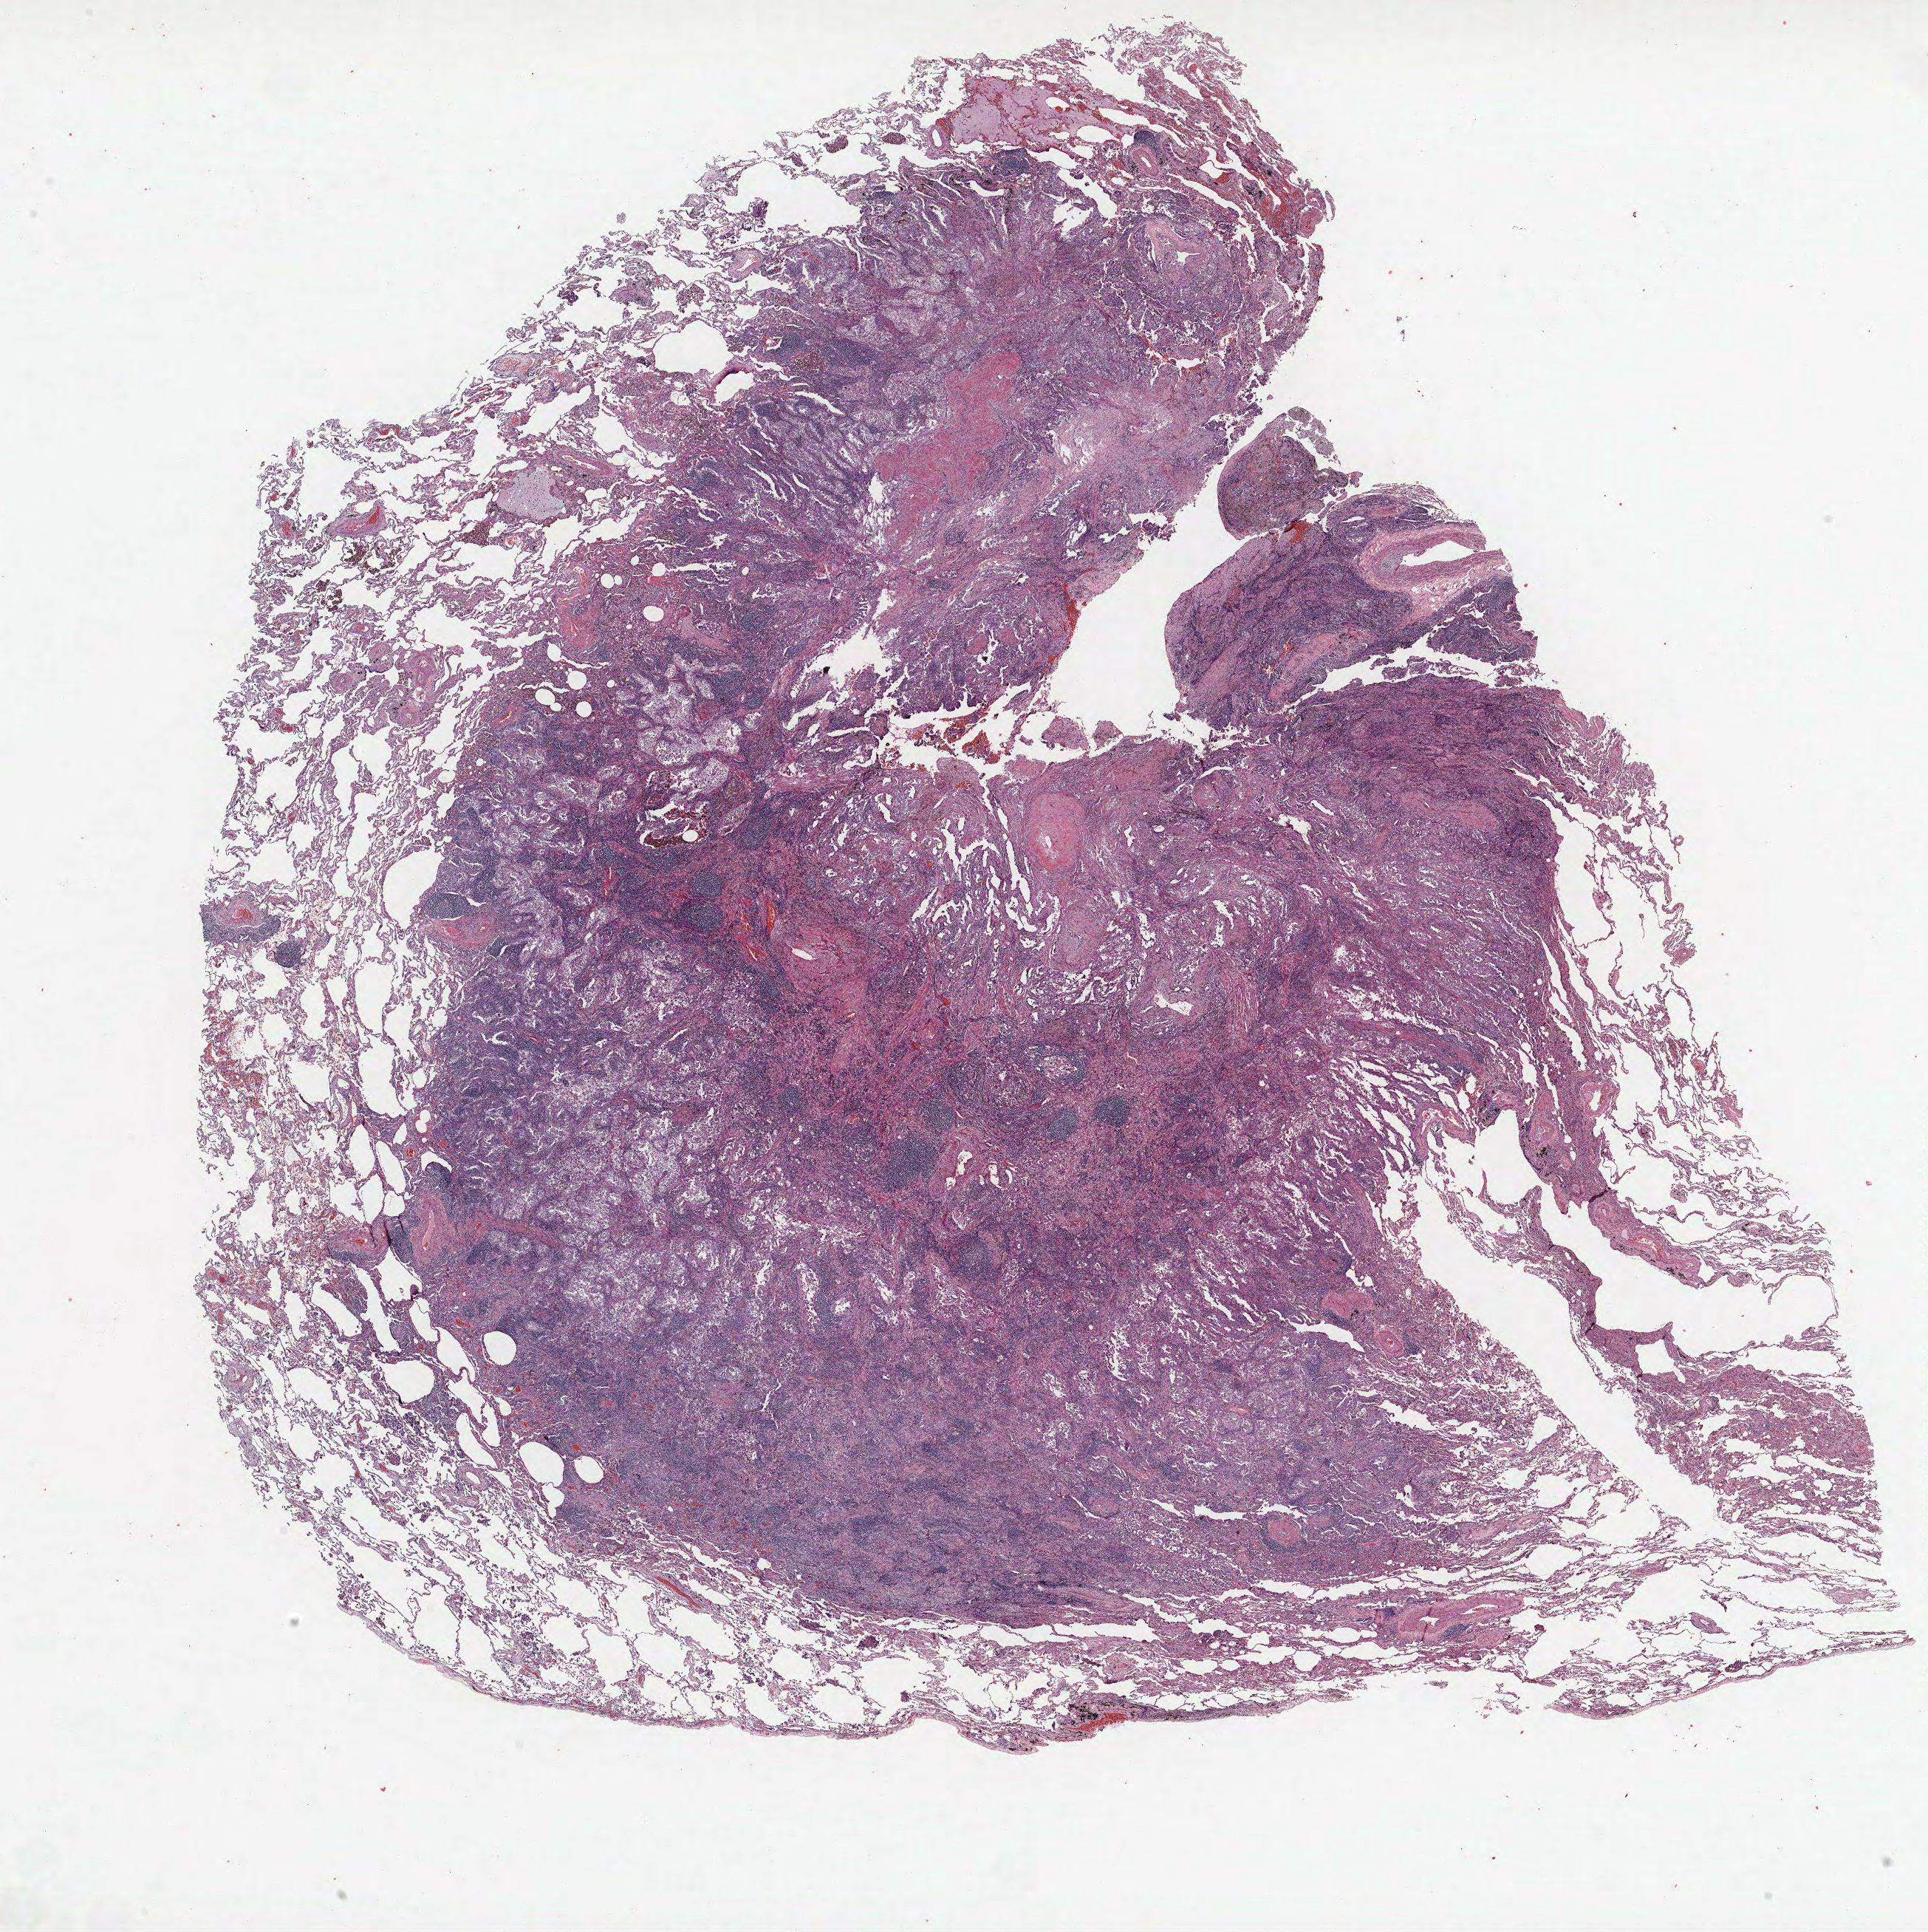
H&E whole-slide image, a low-resolution overview of the entire scanned area, about 20.9 x 20.9 mm (slide scanned at 40x), formalin-fixed paraffin-embedded (FFPE) section, lung. Male, age 63 at enrolment. Current smoker at enrolment. Grade: moderately differentiated (G2).
* tumour size (pathology): 15 mm
* stage (AJCC 6th edition): IA
* participant's lung-cancer diagnosis: Adenocarcinoma, NOS
* primary tumour location (clinical record): left lower lobe